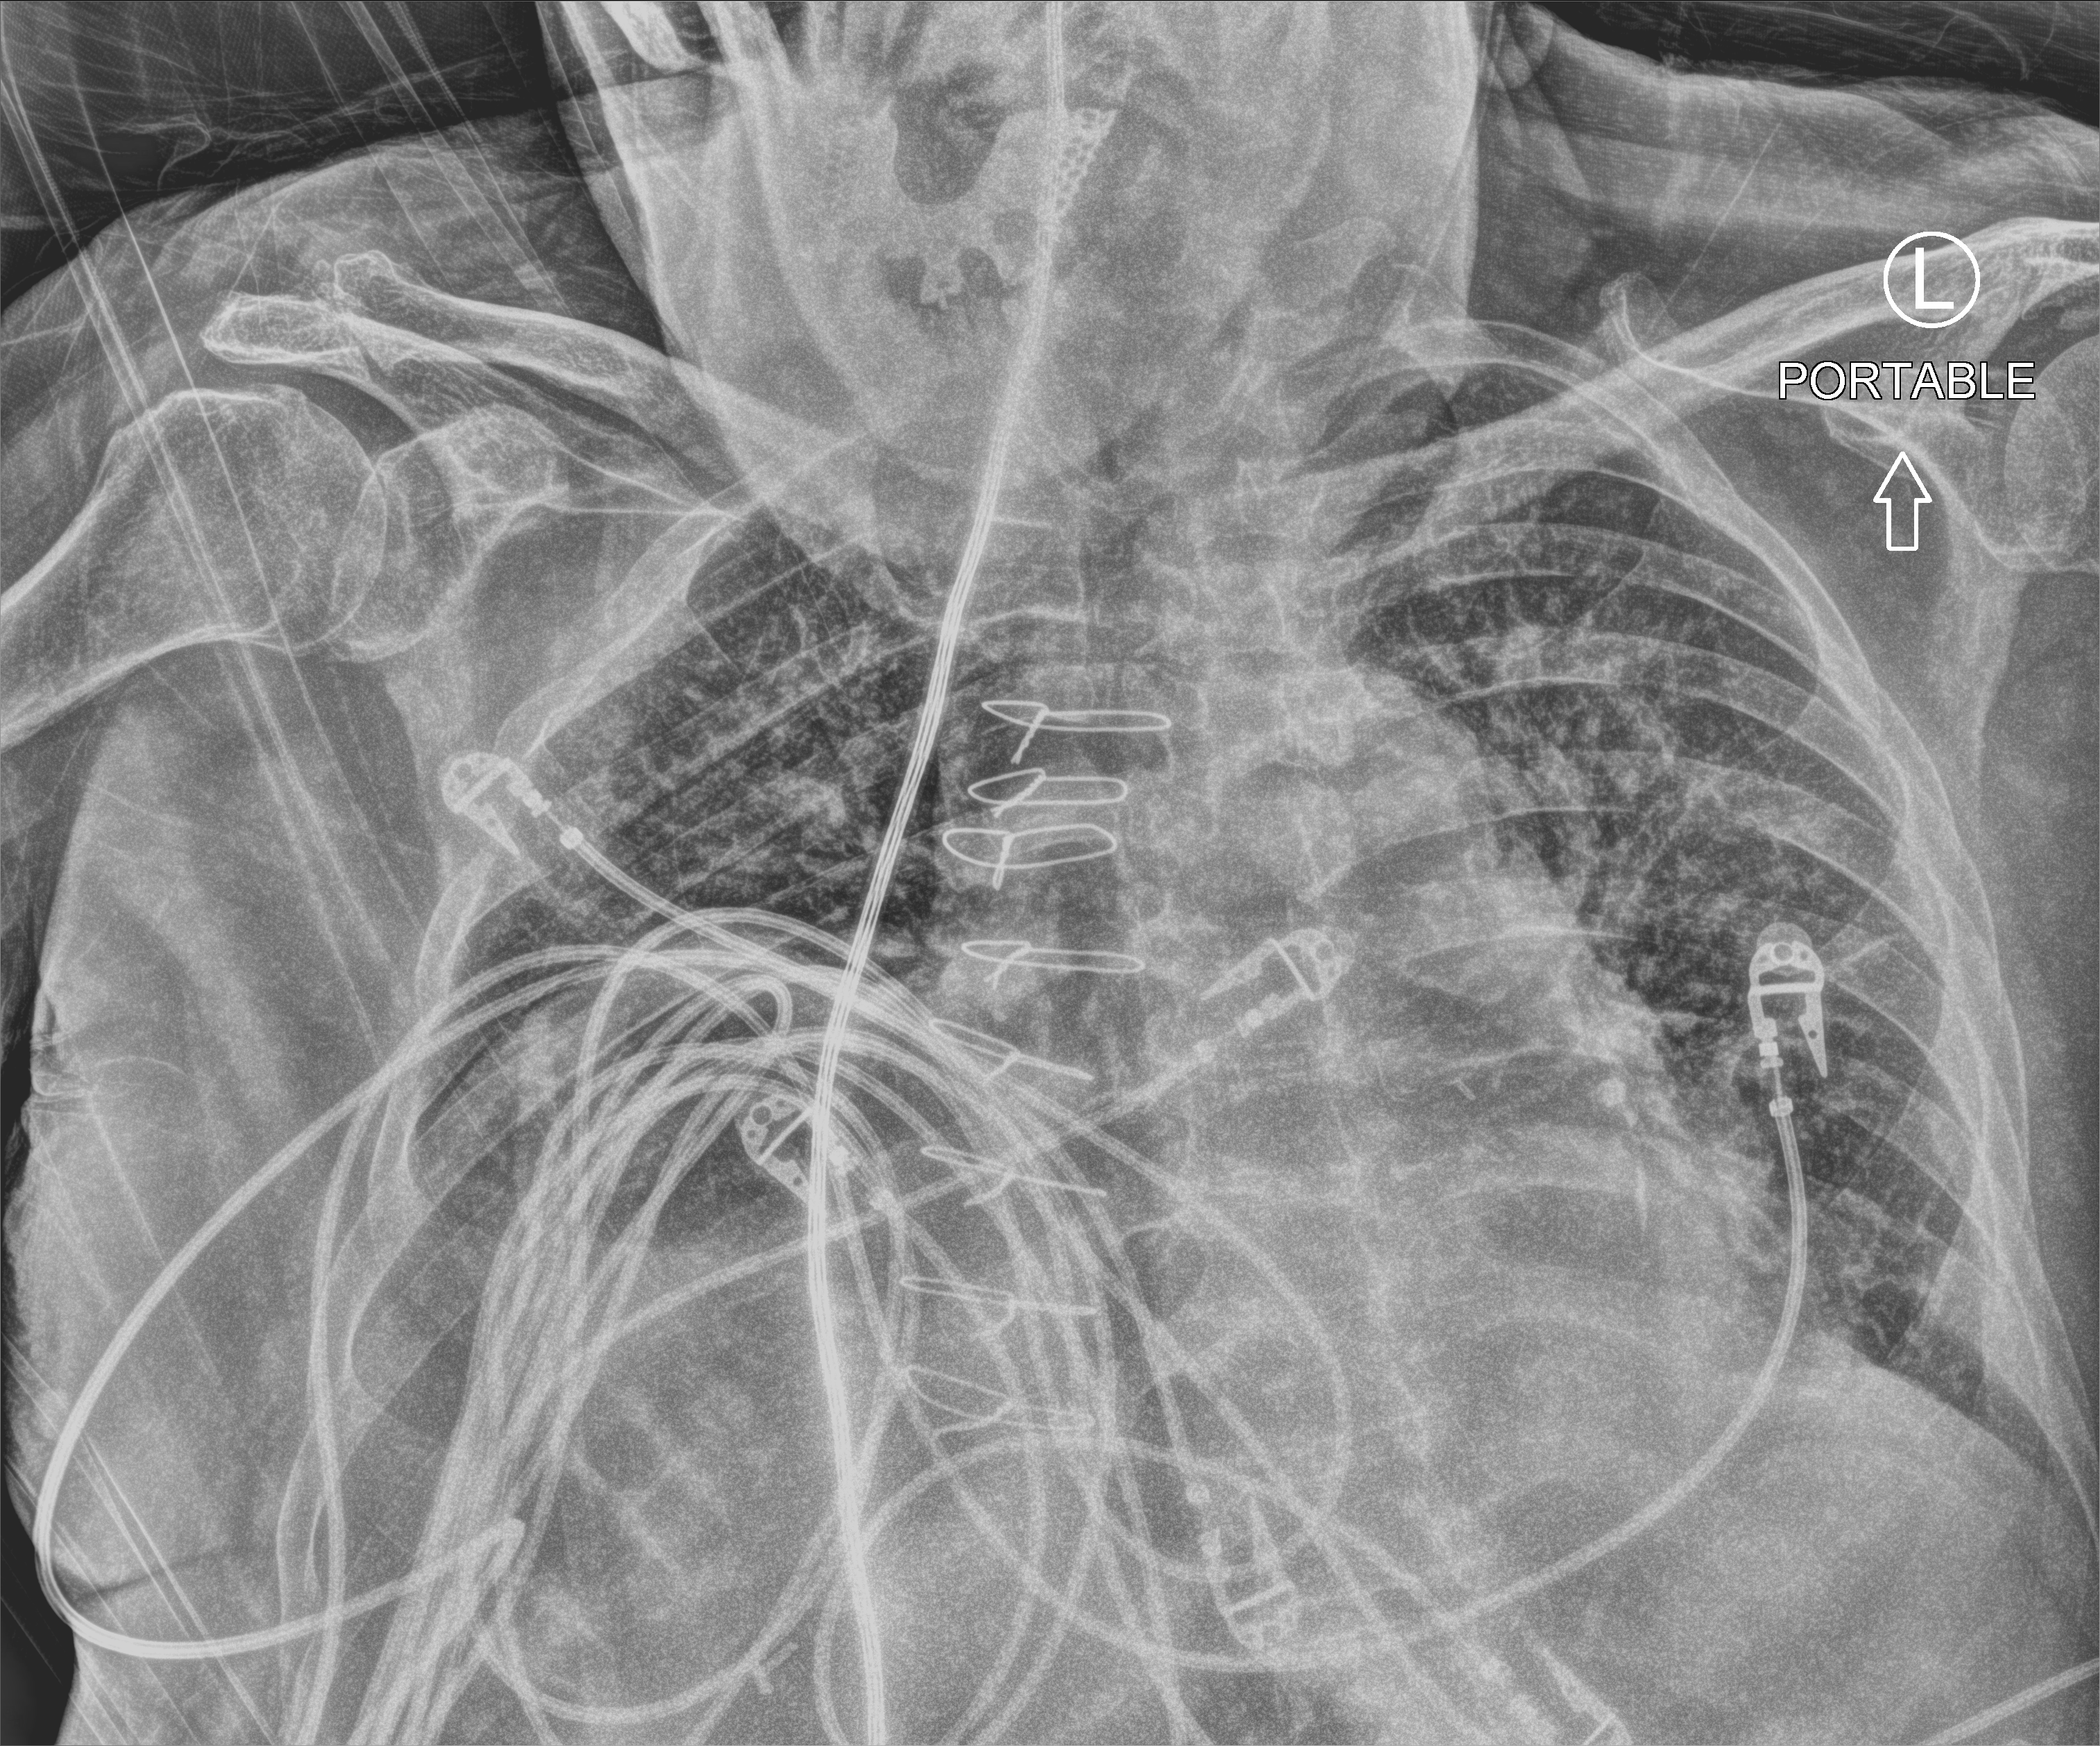
Bedside chest radiograph (computed radiography), anteroposterior (AP) projection. Male patient hospitalised with COVID-19, age 75–90 years.
From the hospital-stay record, not from the radiograph (when in the stay this image was taken is not recorded): smoking status (admission record): former; mechanically ventilated during this hospital stay: no.